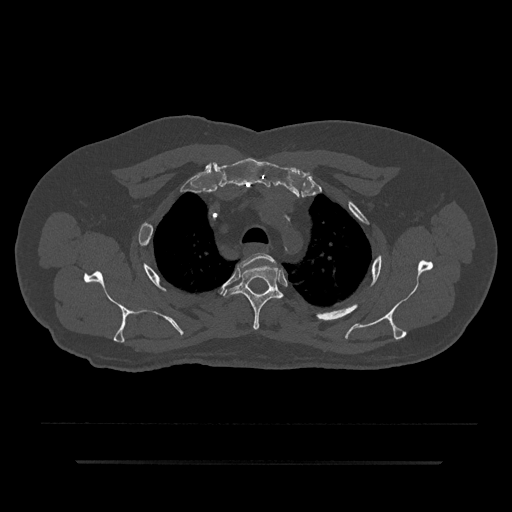
CT including the spine, one axial slice. Slice 661 of 797 in the series (ordered by position). 120 kVp. Bone window (W 1800 / L 400 HU). 0.5 mm slice thickness. 512 × 512 image matrix, field of view 464 × 464 mm. Patient: male, 59 years. From the clinical record (not read from this slice): primary cancer: bile ducts; vertebrae with lytic lesions (as recorded): T10.
Structures marked on this image (semi-automatic segmentation, software-assisted and operator-edited):
- T2 vertebra: bounding box (x1, y1, x2, y2) in pixels: (238, 252, 277, 268)
- T3 vertebra: (223, 265, 283, 330)